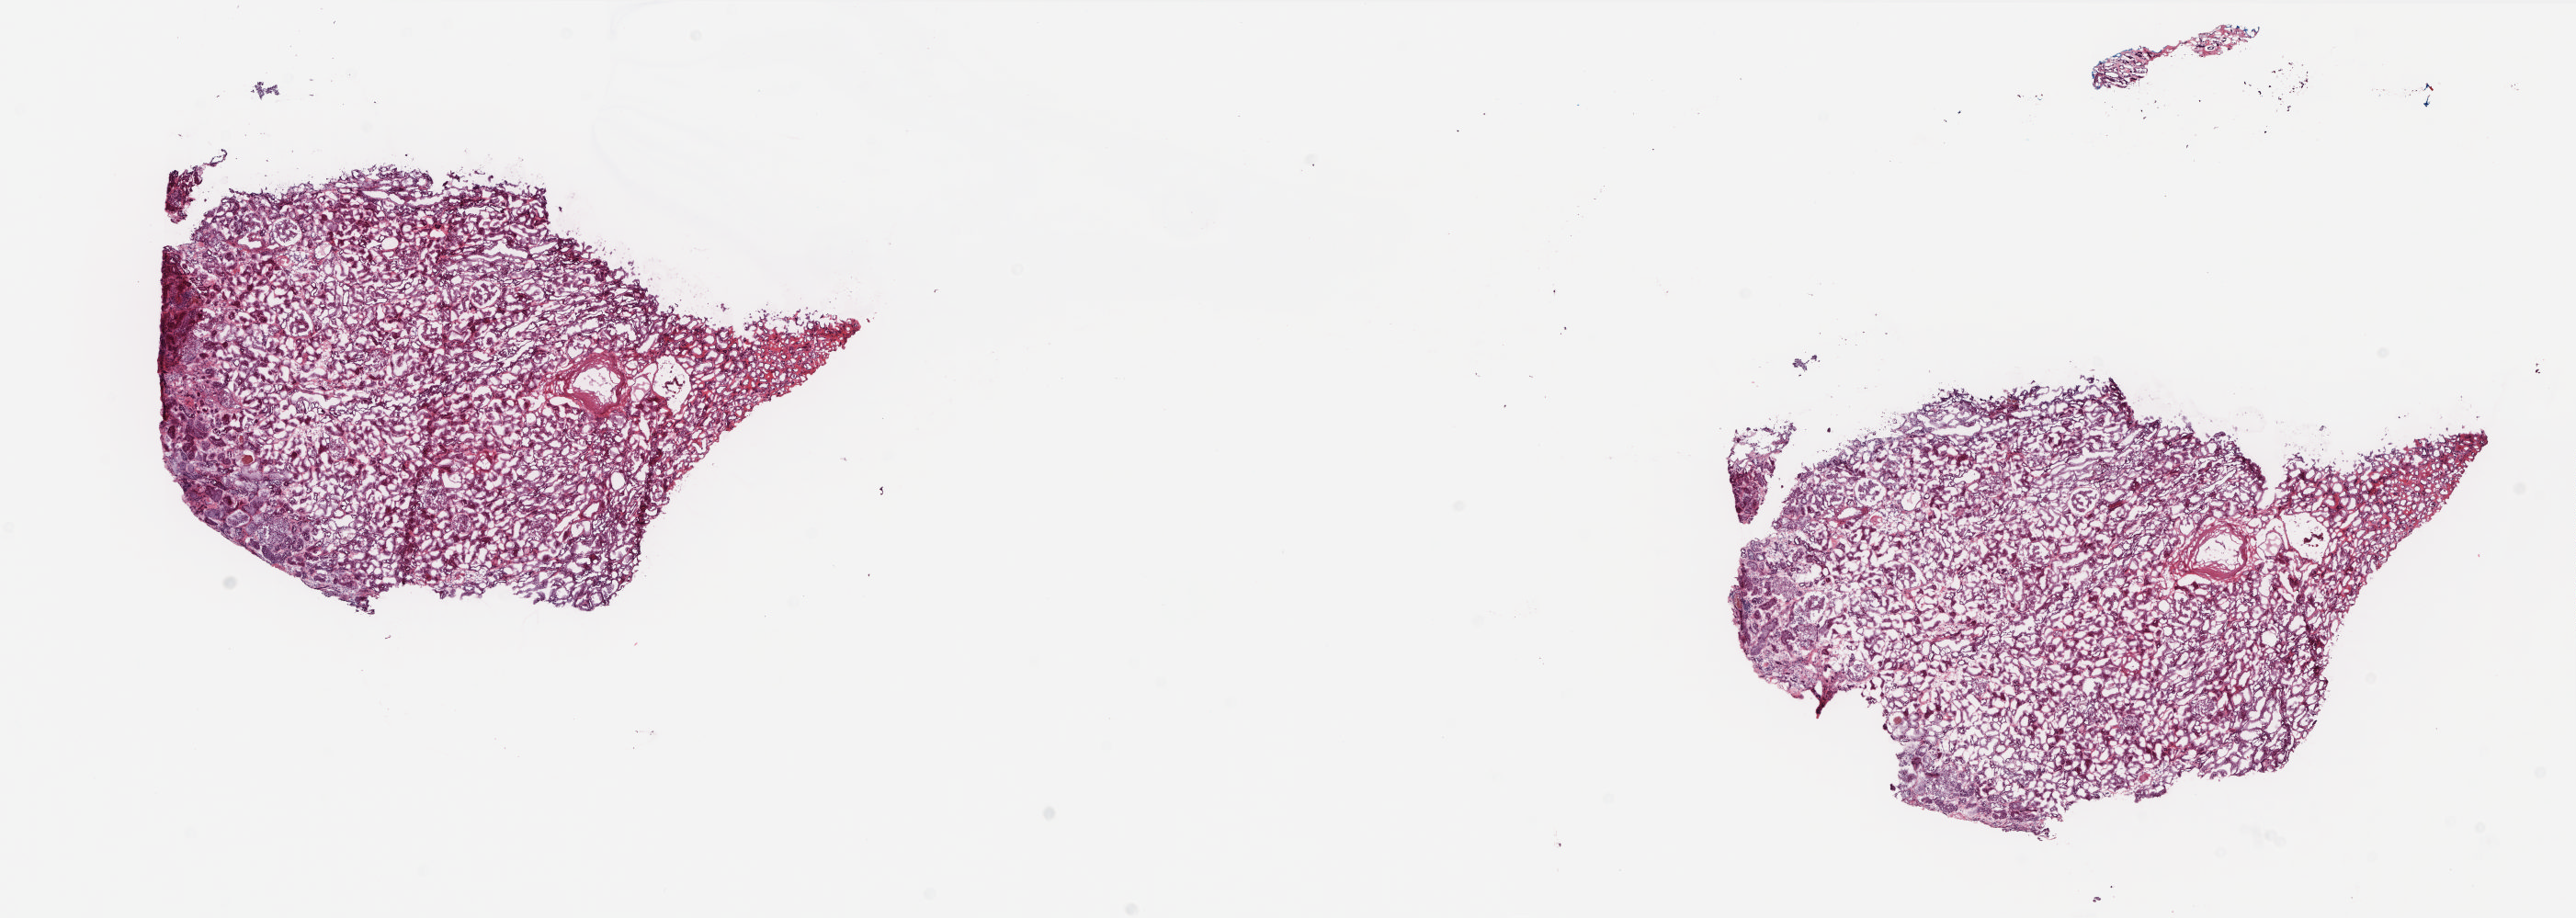
Digitized Hematoxylin and eosin (H&E) stained tissue section (whole slide), whole scanned area (about 22.6 x 8.1 mm) shown as a low-resolution overview. Frozen section from the top of the tissue portion. Kidney, solid tissue normal (non-tumour tissue) sample. Patient: male, age at initial diagnosis 85 years. Pathologist review of this section (percent, as recorded): tumour cells 0%, tumour nuclei 0%, normal cells 65%, stromal cells 35%, necrosis 0%. Inflammatory infiltration, as recorded: lymphocyte infiltration 2%, monocyte infiltration 3%, neutrophil infiltration 0%.
This section: solid tissue normal (non-tumour) sample from the same patient. Patient diagnosis: Papillary adenocarcinoma, NOS.